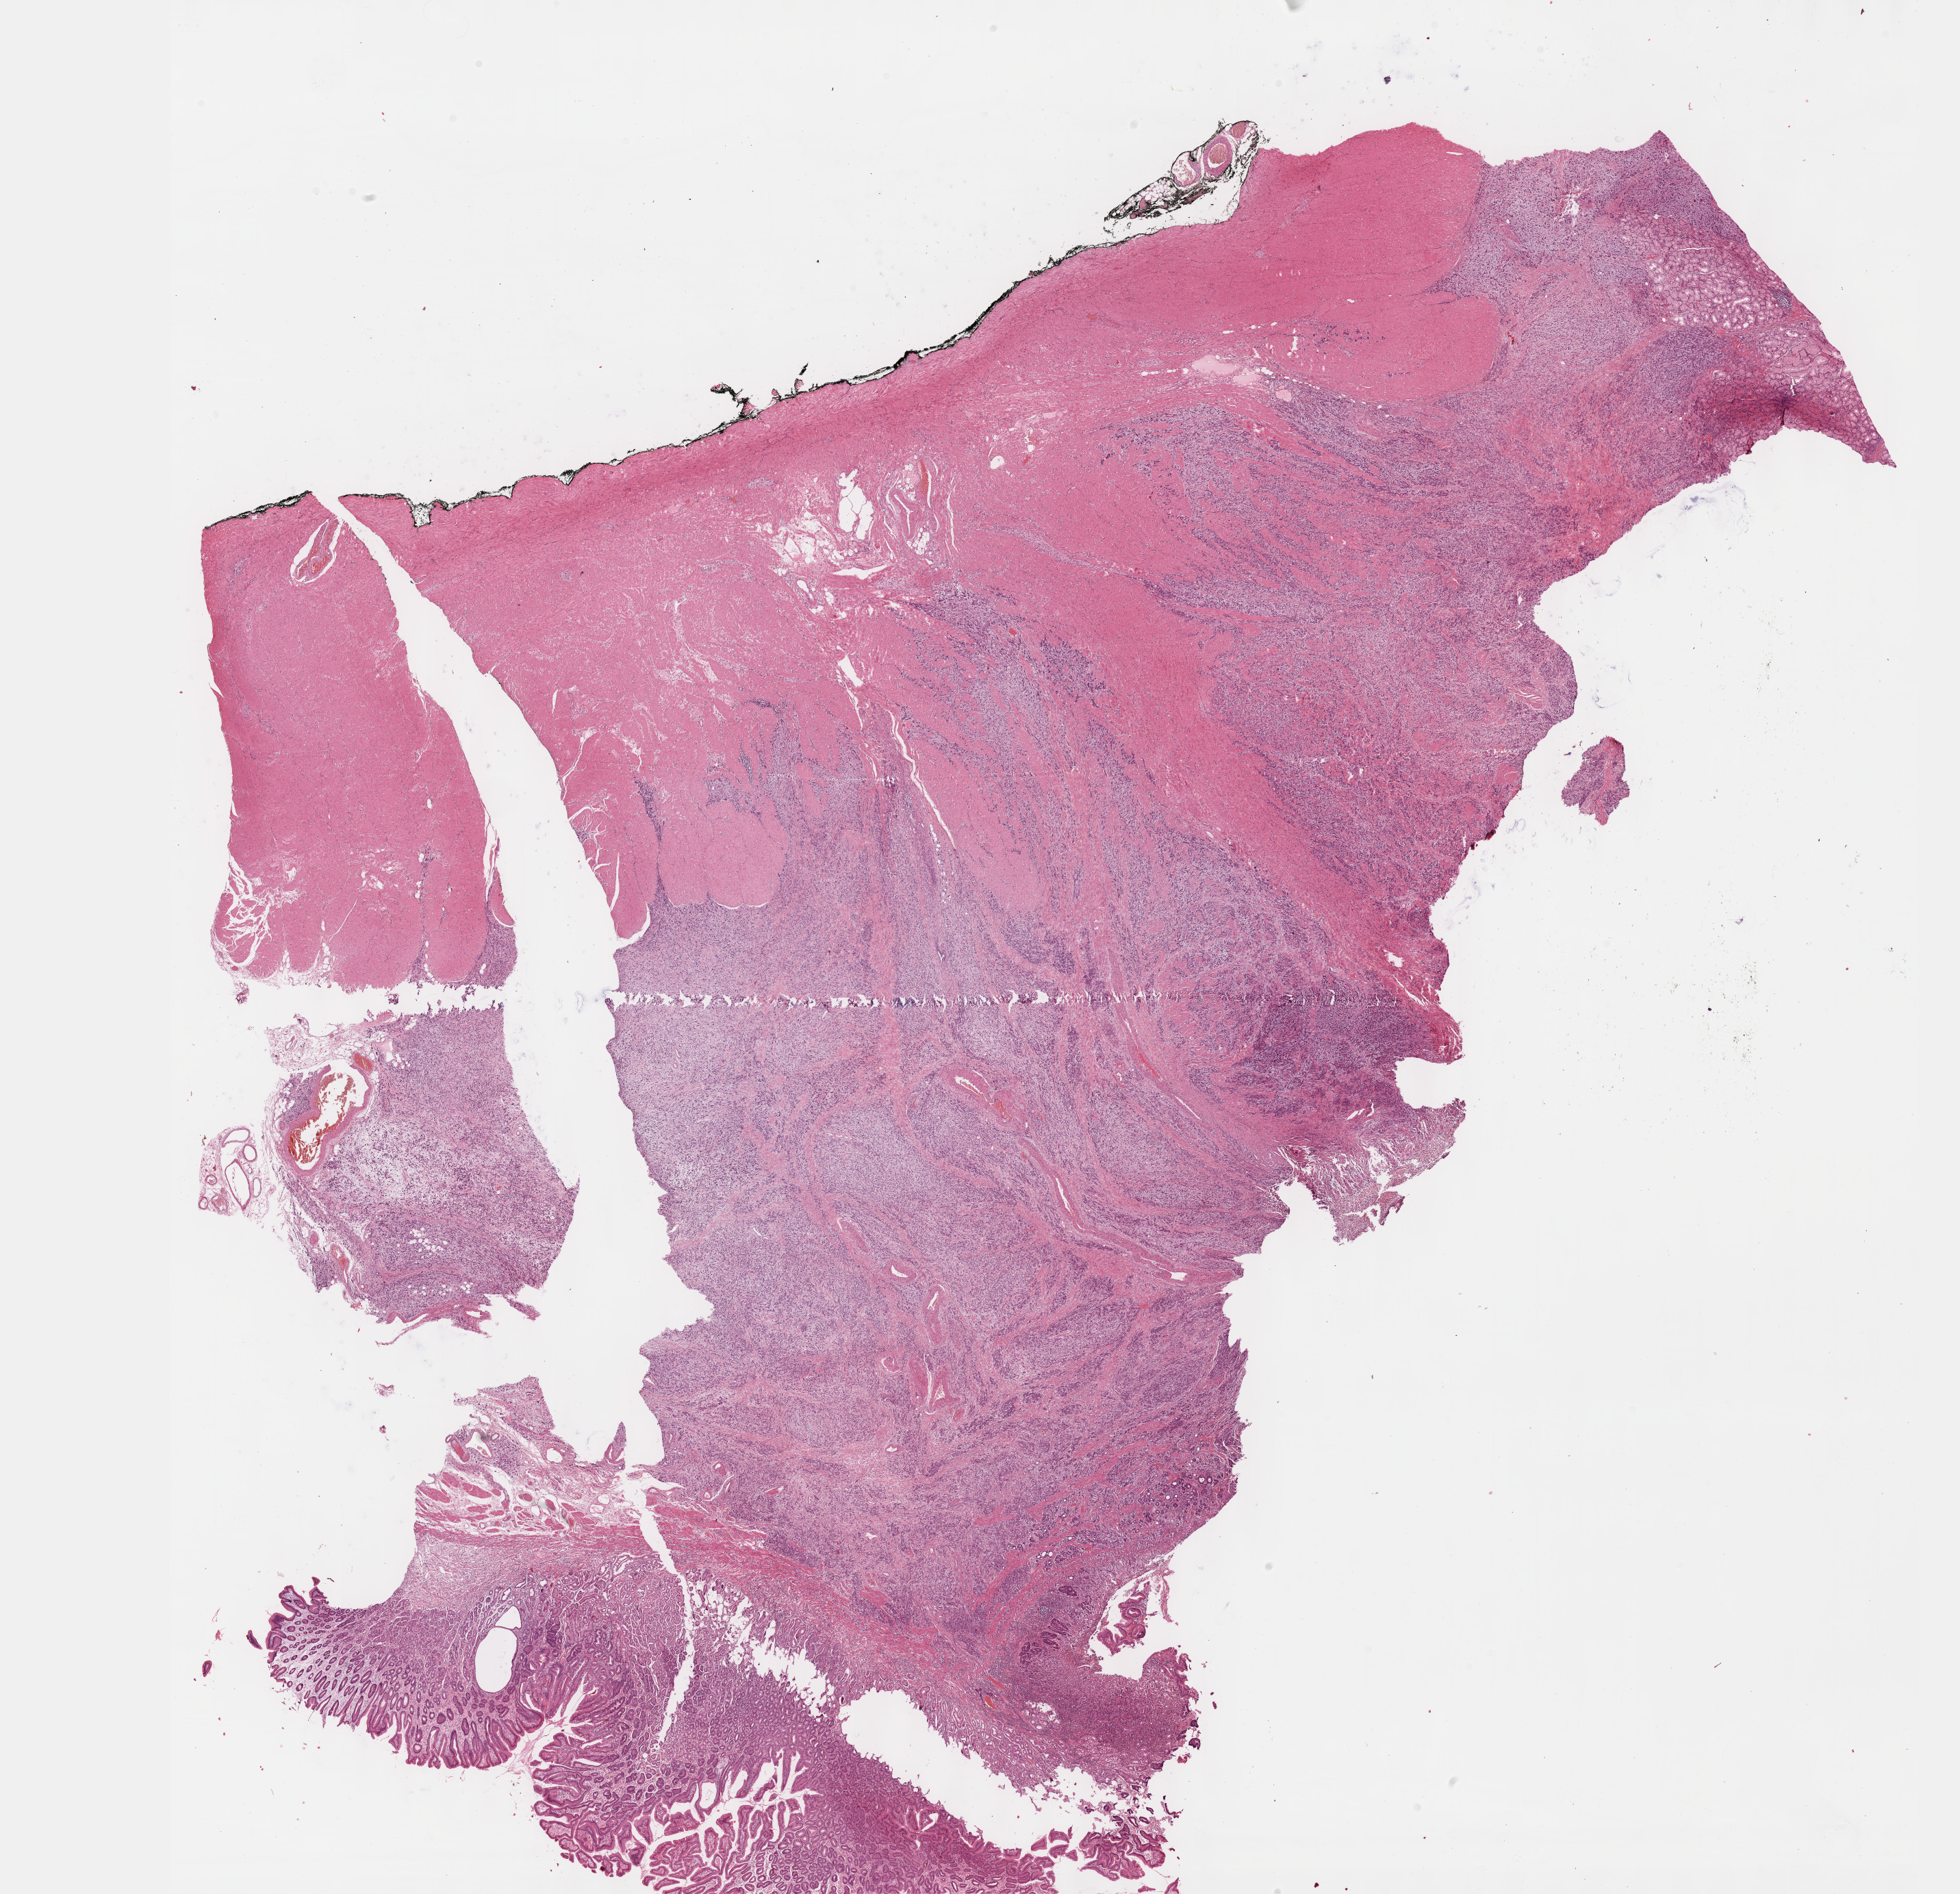
Digitized H&E tissue section (whole slide), shown as a low-resolution overview of the whole scanned area (about 23.1 x 22.4 mm, acquisition: 40x scan); formalin-fixed paraffin-embedded (FFPE) diagnostic section; sample: primary tumour, stomach. Patient: male, age at initial diagnosis 65 years.
Pathologic diagnosis: Signet ring cell carcinoma (gastric antrum).